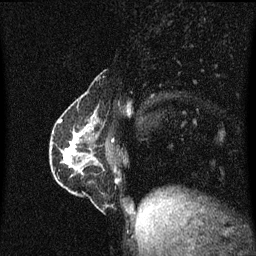
Breast MRI (dynamic contrast-enhanced), one sagittal slice. Slice 20 of 60 in the series (ordered by position). Dynamic contrast-enhanced series, image 2 of 3 at this slice position (ordered by acquisition). 1.5 T. TE 4.2 ms, TR 8.4 ms. 2 mm slice thickness. 256 × 256 image matrix, field of view 200 × 200 mm. Patient: female, 40 years.
Structures marked on this image (semi-automatic segmentation, software-assisted and operator-edited):
- analysis volume of interest (the breast-tissue region the enhancement analysis was run in; not a lesion): bounding box (x1, y1, x2, y2) in pixels: (57, 110, 113, 191)
- tumour enhancement mask (voxels above the 70 % enhancement threshold inside the analysis volume of interest): (59, 120, 82, 165)